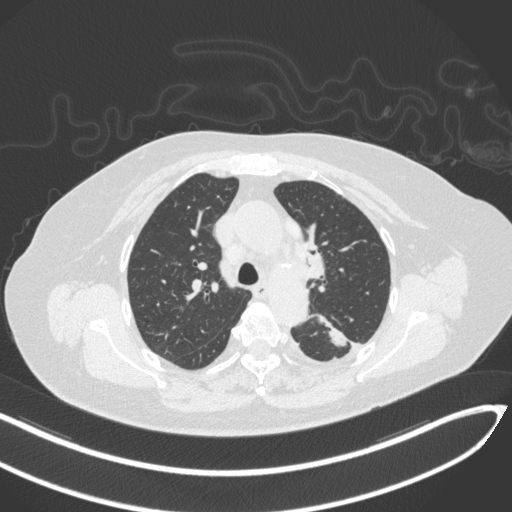
Chest CT, one axial slice; 120 kVp; lung window (W 1500 / L -600 HU); 512 × 512 image matrix. Female patient, age 76 years. Case-level facts recorded for this patient, not image findings: clinical TNM (as recorded): T1c N0 M0.
Outlined on this slice (bounding box drawn by a radiologist):
- lung tumour (recorded histology: adenocarcinoma): bounding box [x1, y1, x2, y2] px = [313, 308, 357, 350]